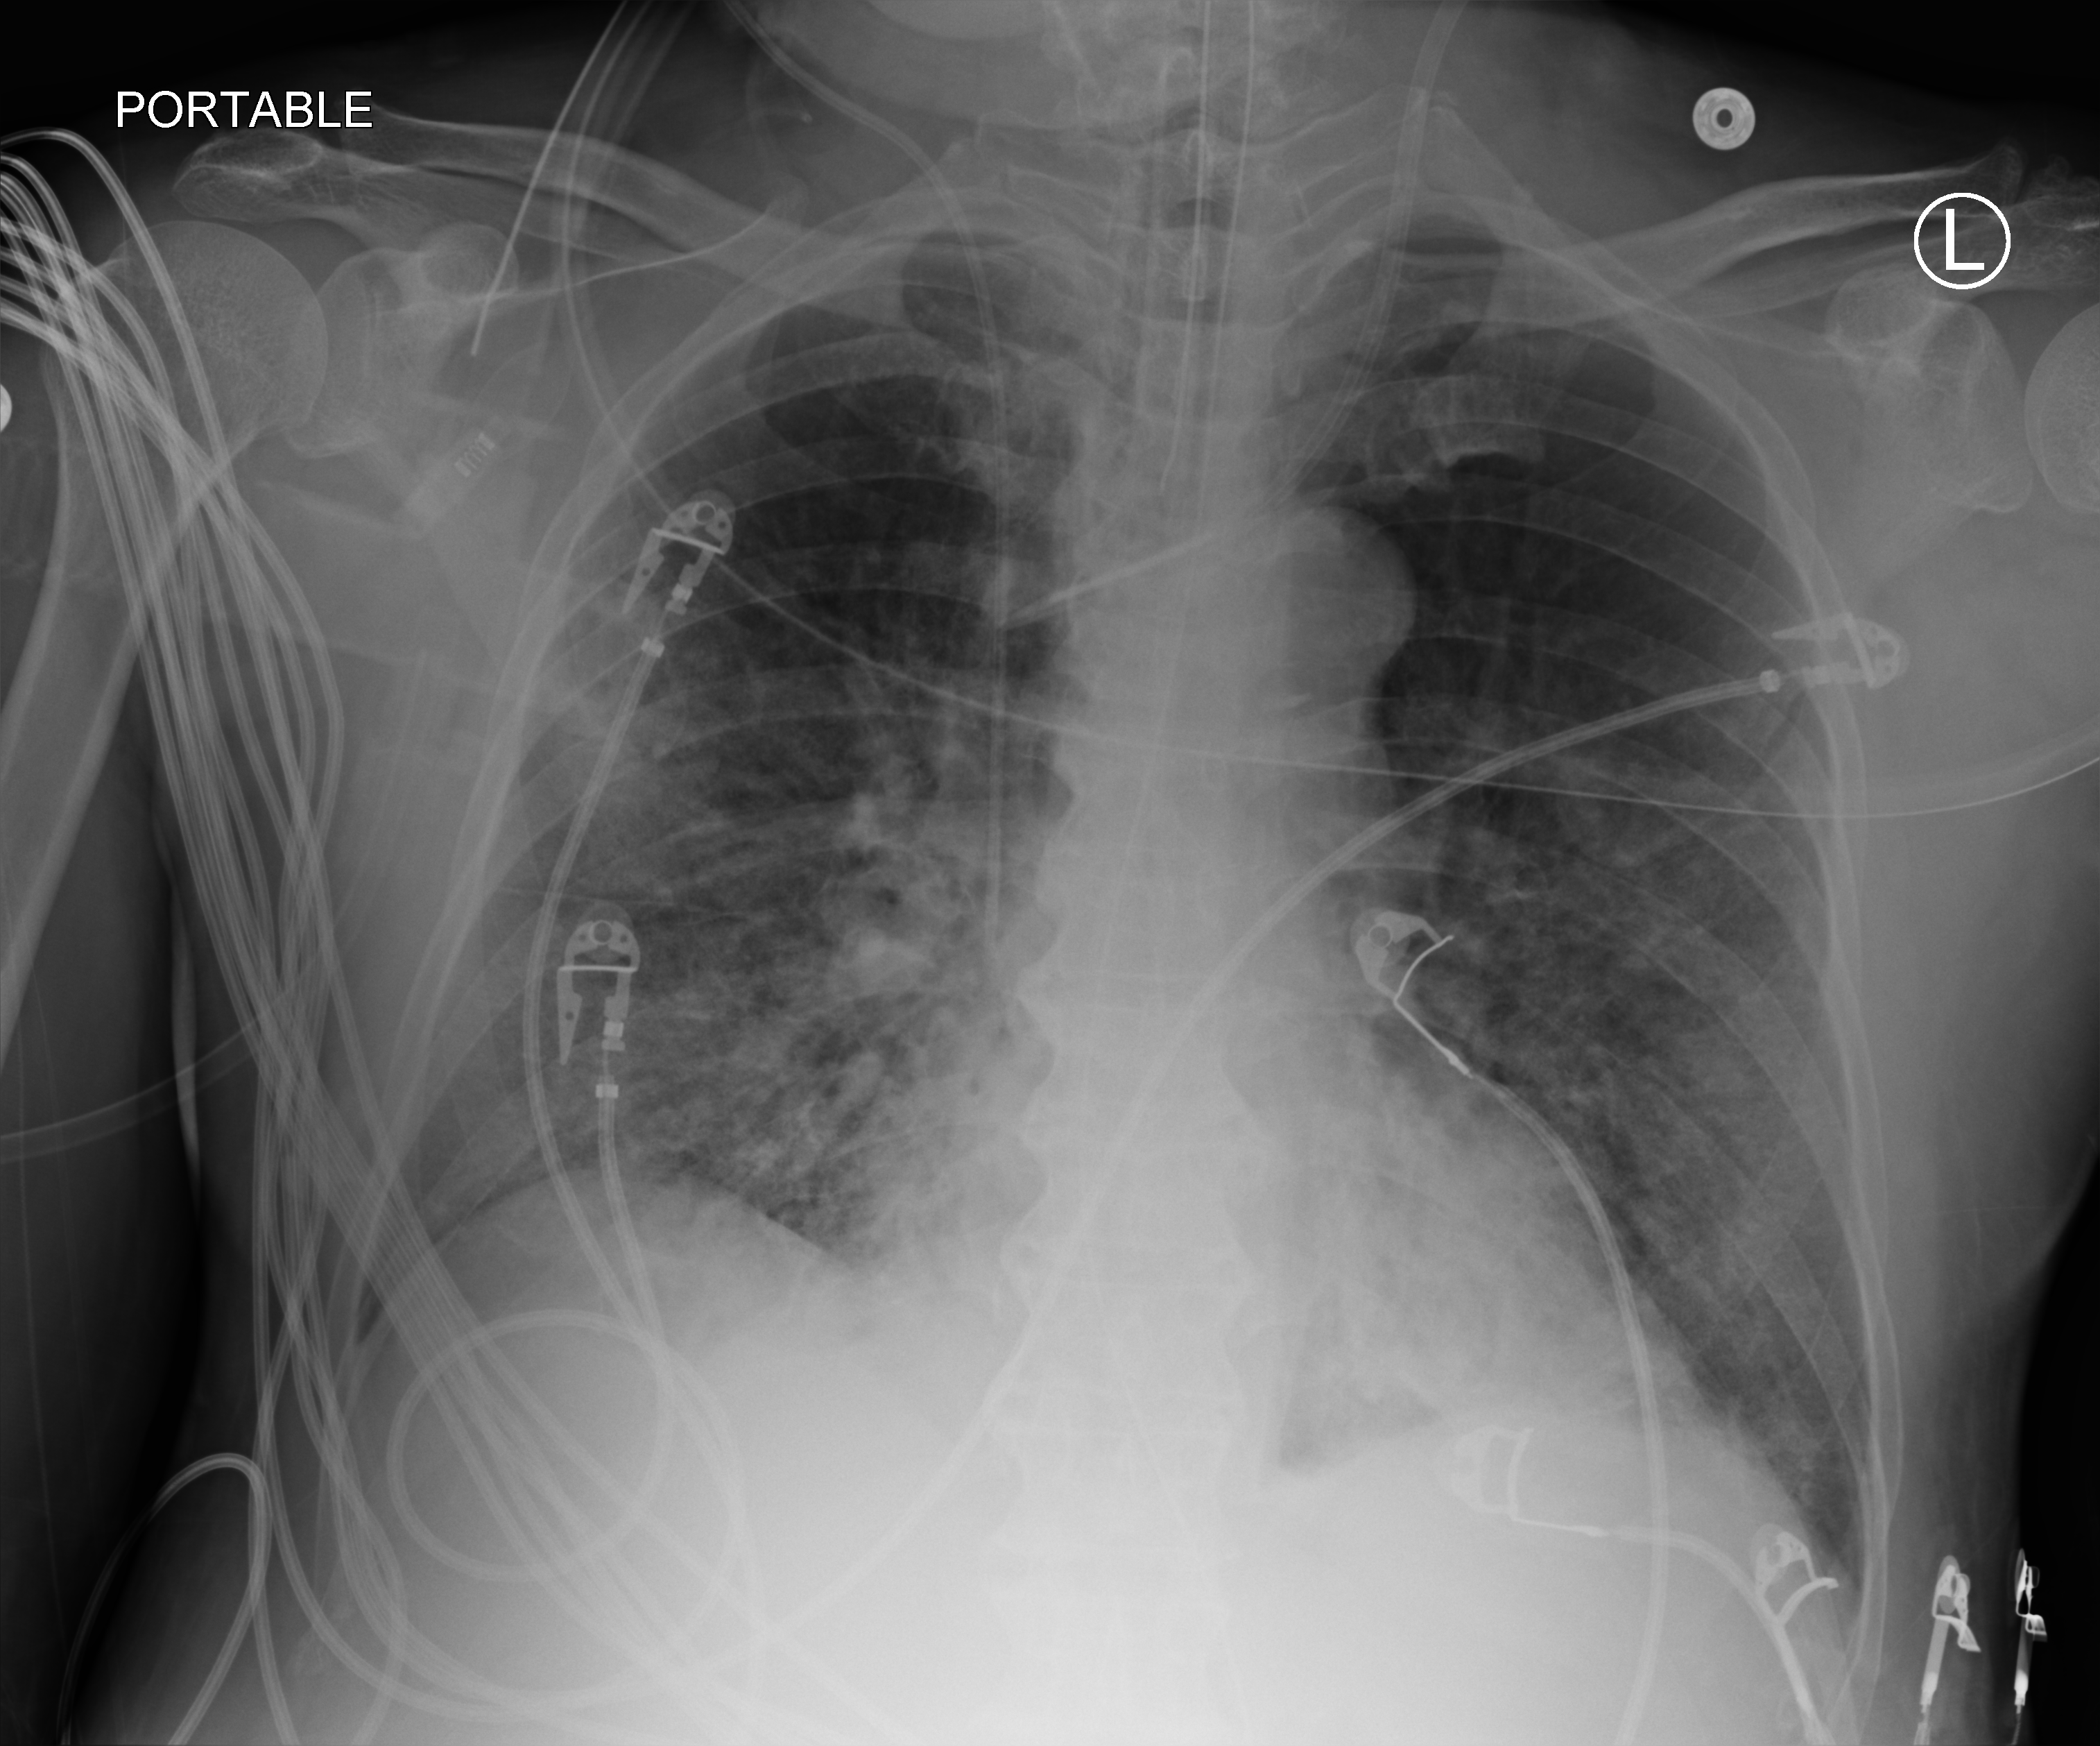
Bedside chest radiograph (computed radiography), anteroposterior (AP) projection. Male patient hospitalised with COVID-19, age 60–74 years.
From the hospital-stay record, not from the radiograph (when in the stay this image was taken is not recorded):
- chronic kidney disease (admission record): no